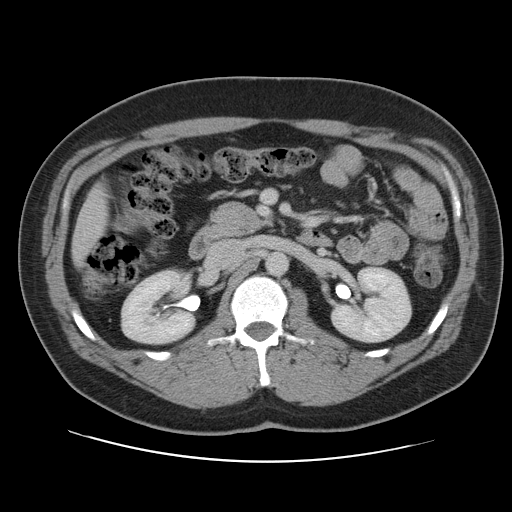
Contrast-enhanced abdominal CT, one axial slice. Intravenous contrast given. Soft-tissue window (W 400 / L 40 HU). 512 × 512 image matrix, field of view 402 × 402 mm. Male patient, age 35 years. From the clinical record (not read from this slice): diagnosis: colorectal cancer liver metastases, imaged before liver resection.
Outlined on this slice (outlined manually by an expert reader):
- liver: bounding box (x1, y1, x2, y2) in pixels: (73, 187, 108, 260)
- planned liver remnant (the part of the liver to remain after resection): (73, 187, 107, 260)